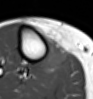
MRI of an extremity soft-tissue mass, one axial slice. Slice 30 of 54 in the series (ordered by position). MR volume resampled by the dataset authors to the PET/CT grid (not the native acquisition matrix). 3.27 mm slice thickness. 93 × 99 image matrix, field of view 91 × 97 mm. Female patient. From the clinical record (not read from this slice): histological type: undifferentiated – high grade; grade: high; site of the primary tumour: right thigh.
Structures marked on this image (expert contour drawn on MRI and transferred to this co-registered scan by the dataset authors):
- gross tumour volume (mass): box from (x=41, y=41) to (x=69, y=74) px